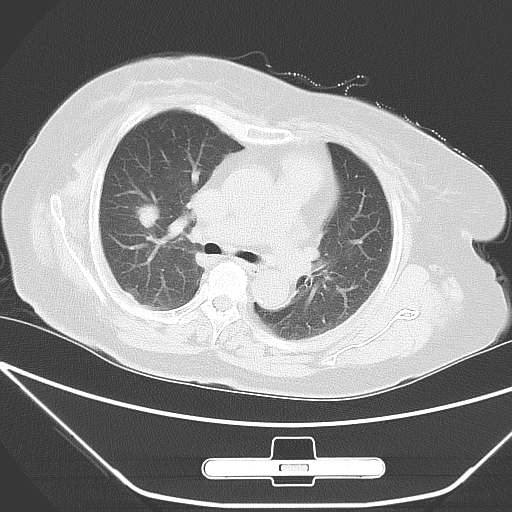
Chest CT, one axial slice; slice 33 of 49 in the series (ordered by position); 120 kVp; lung window (W 1500 / L -600 HU); 5 mm slice thickness; 512 × 512 image matrix, field of view 365 × 365 mm. Female patient, age 65 years. From the clinical record (not read from this slice): clinical TNM (as recorded): T1c N0 M0.
Annotated regions visible in this slice (bounding box drawn by a radiologist):
- lung tumour (recorded histology: adenocarcinoma): bounding box (x1, y1, x2, y2) in pixels: (131, 199, 169, 233)